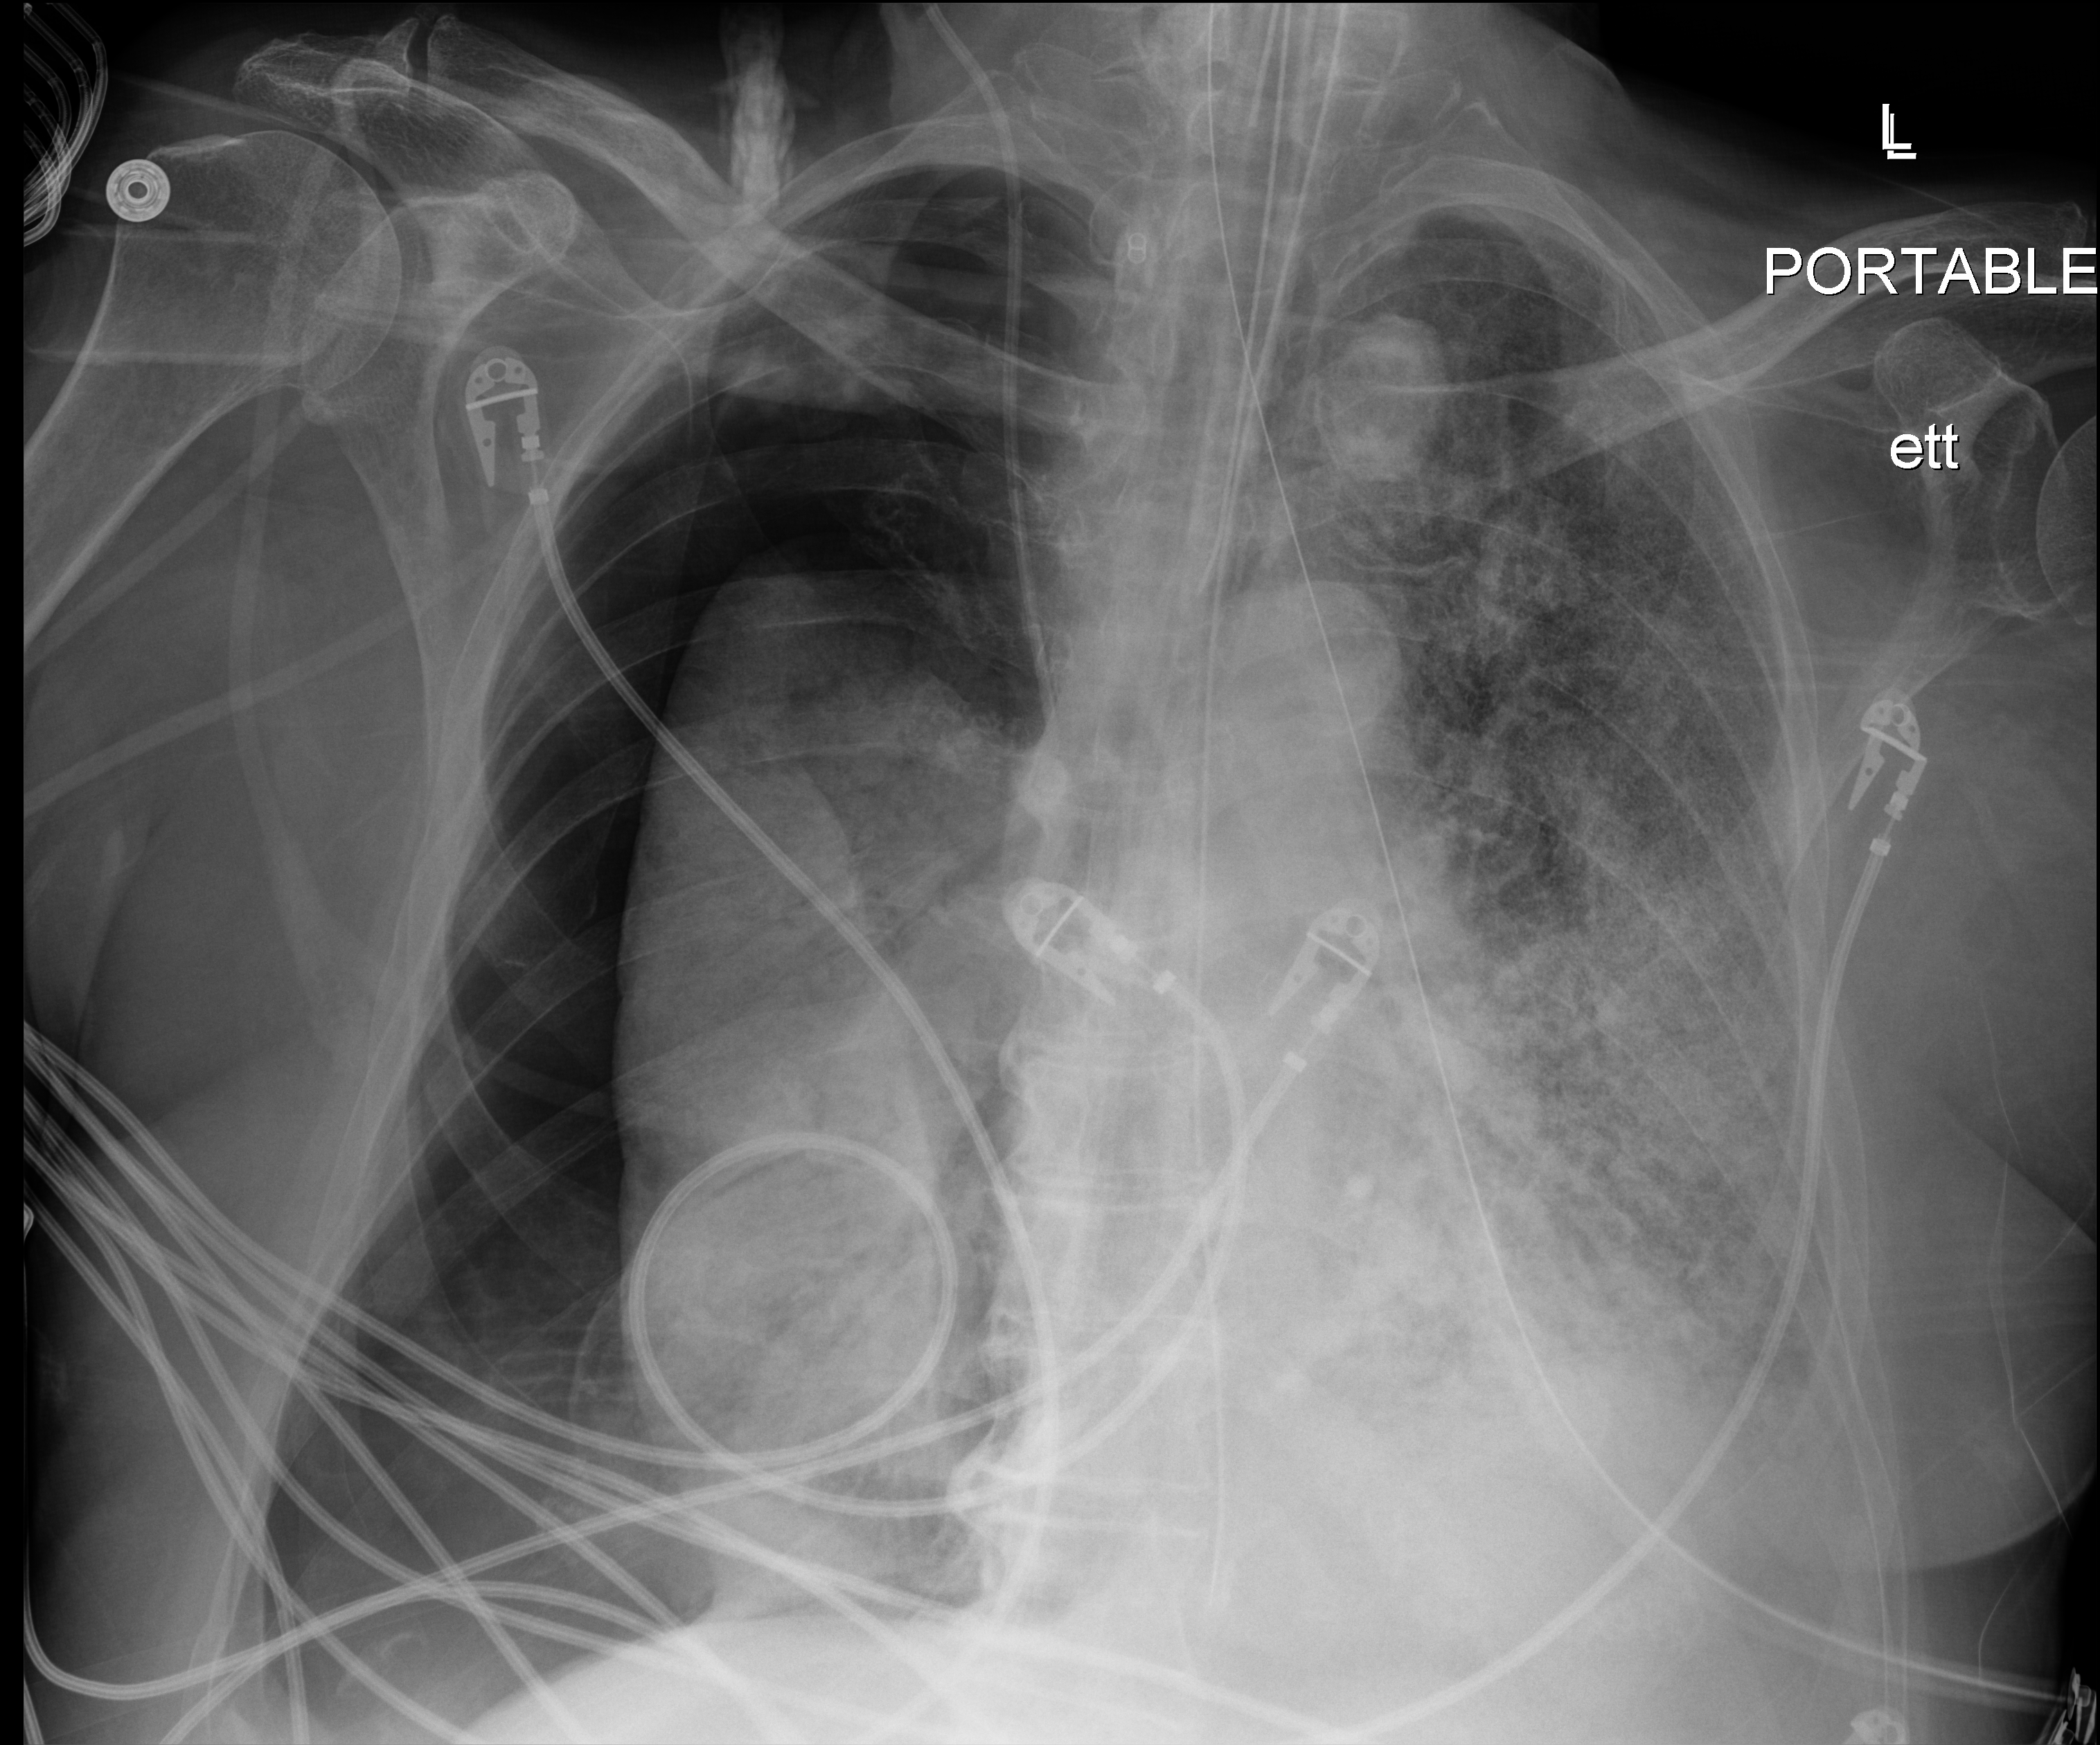
Chest X-ray (portable). Male patient hospitalised with COVID-19, age 75–90 years.
Hospital-stay facts (about this admission, not read from this image; timing relative to this image not recorded):
- mechanically ventilated during this hospital stay: yes
- admitted to intensive care during this hospital stay: yes
- hypertension (admission record): no